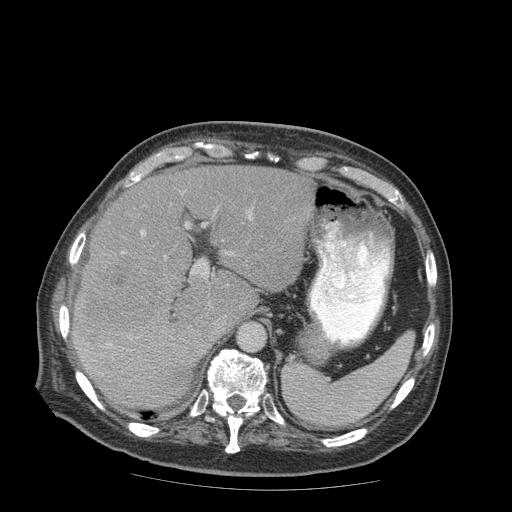
Contrast-enhanced abdominal CT (liver protocol), one axial slice; position 60 of 99 along the scan axis; reconstruction kernel STANDARD; soft-tissue window (W 400 / L 40 HU); 512 × 512 image matrix, field of view 420 × 420 mm. From the clinical record (not read from this slice): diagnosis: hepatocellular carcinoma (patient treated with transarterial chemoembolisation; whether this scan precedes or follows treatment is not stated here); TNM stage (as recorded): Stage-IIIB; Child-Pugh class: A; tumour differentiation: well differentiated.
Annotated regions visible in this slice (semi-automatically segmented with operator editing):
- liver parenchyma outside the tumour (the mass and vessels are separate outlines, so this box may not span the whole liver): bounding box [x1, y1, x2, y2] px = [72, 166, 312, 408]
- mass: [75, 251, 165, 337]
- liver vessels: [86, 210, 252, 366]